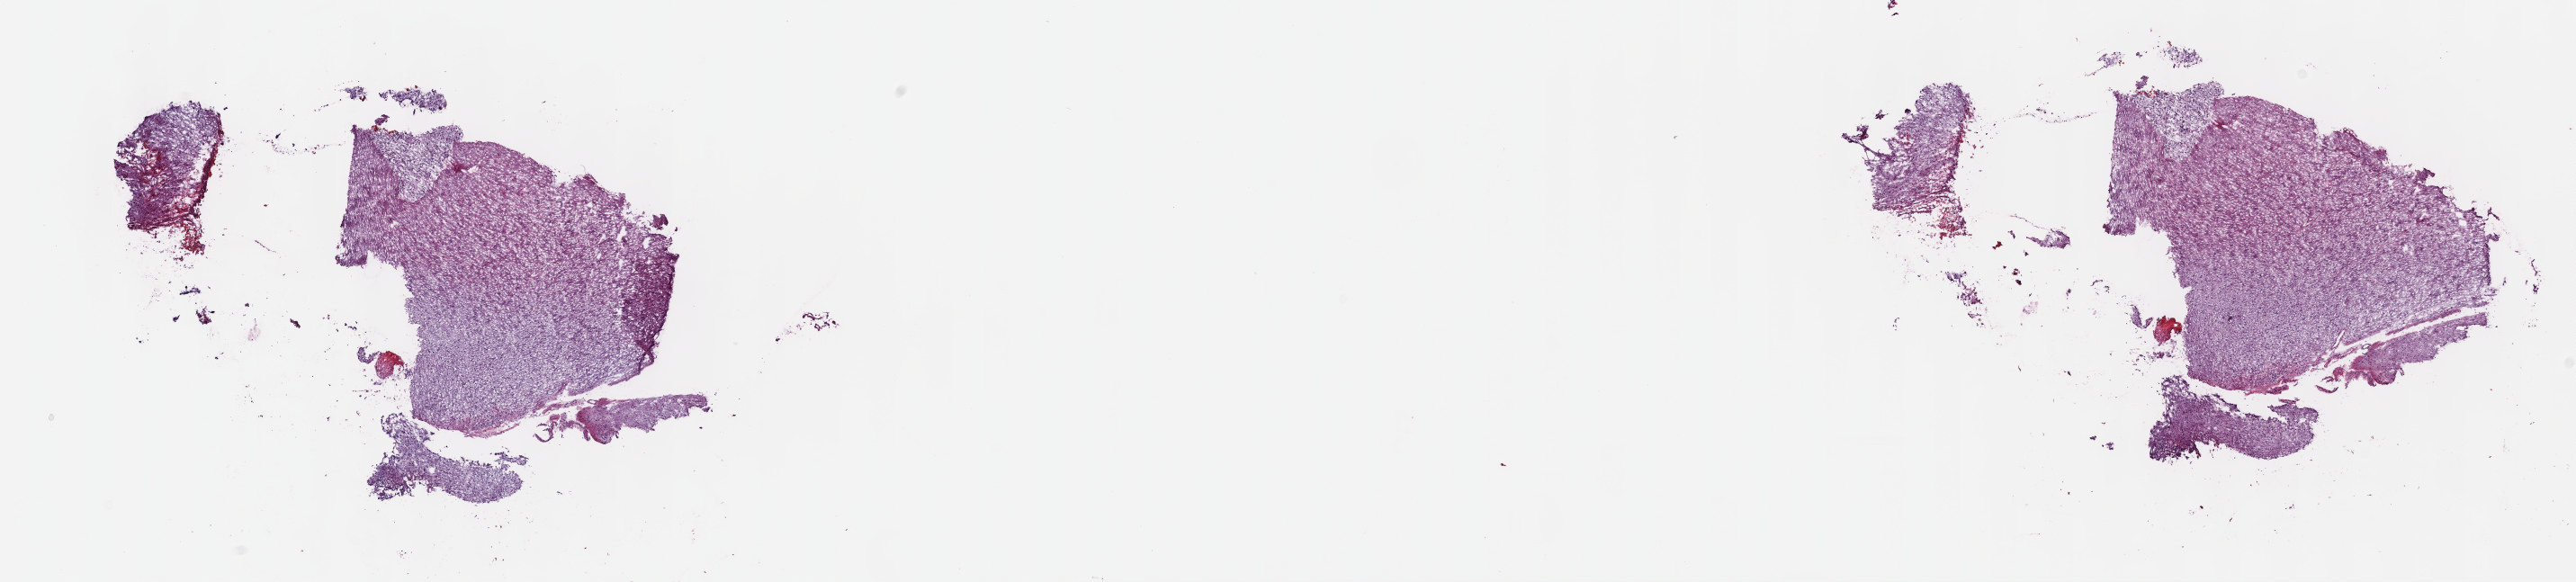
Whole-slide histology image, Hematoxylin and eosin (H&E) stained, a low-resolution overview of the entire scanned area, about 23.2 x 5.2 mm. Frozen section. Brain, primary tumour sample. Patient: male, age at initial diagnosis 32 years. Histologic grade: G3 (poorly differentiated). Pathologist review of this section (percent, as recorded): tumour cells 40%, tumour nuclei 80%, normal cells 20%, stromal cells 40%, necrosis 0%. Infiltration values recorded for this section: lymphocyte infiltration 0%, monocyte infiltration 0%, neutrophil infiltration 0%.
Diagnosis: Astrocytoma, anaplastic (cerebrum).